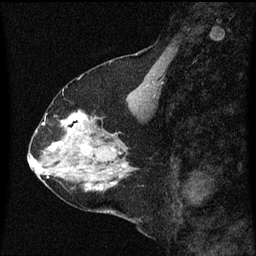
Breast MRI (dynamic contrast-enhanced), one sagittal slice; position 24 of 60 along the scan axis; dynamic contrast-enhanced series, image 2 of 3 at this slice position (ordered by acquisition); 1.5 T; TE 4.2 ms, TR 8 ms; 2 mm slice thickness; 256 × 256 image matrix. Patient: female, 58 years.
Outlined on this slice (semi-automatically segmented with operator editing):
- analysis volume of interest (the breast-tissue region the enhancement analysis was run in; not a lesion): bounding box [x1, y1, x2, y2] px = [56, 112, 99, 149]
- tumour enhancement mask (voxels above the 70 % enhancement threshold inside the analysis volume of interest): [58, 112, 89, 147]